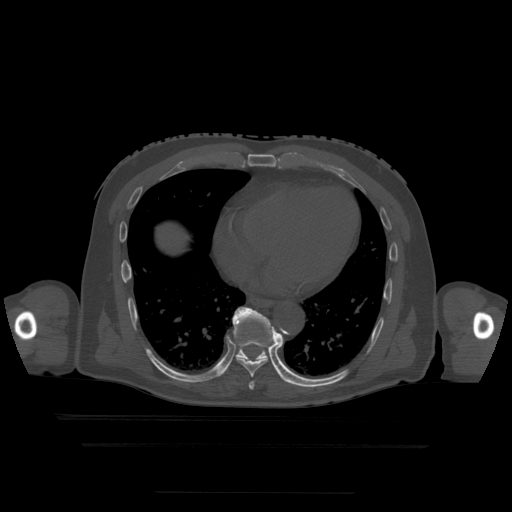
CT including the spine, one axial slice. Position 273 of 522 along the scan axis. Bone window (W 1800 / L 400 HU). 1.25 mm slice thickness. 512 × 512 image matrix, field of view 436 × 436 mm. Patient age 68 years. Case-level facts recorded for this patient, not image findings: primary cancer: urothelial.
Outlined on this slice (semi-automatically segmented with operator editing):
- T7 vertebra: bounding box <249,382,255,390> (left, top, right, bottom; pixels)
- T8 vertebra: <237,308,275,378>
- T9 vertebra: <223,307,281,377>